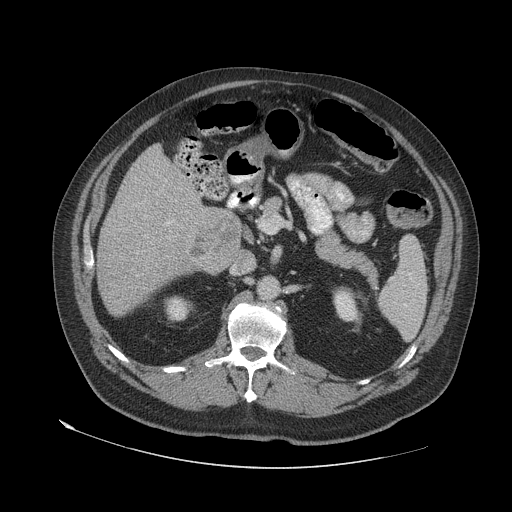
Contrast-enhanced abdominal CT (liver protocol), one axial slice. Reconstruction kernel STANDARD. Soft-tissue window (W 400 / L 40 HU). 2.5 mm slice thickness. 512 × 512 image matrix. Case-level facts recorded for this patient, not image findings: diagnosis: hepatocellular carcinoma (patient treated with transarterial chemoembolisation; whether this scan precedes or follows treatment is not stated here); TNM stage (as recorded): Stage-IVA; Child-Pugh class: A; tumour differentiation: well differentiated; tumour nodularity: multinodular.
Structures marked on this image (semi-automatic segmentation, software-assisted and operator-edited):
- liver parenchyma outside the tumour (the mass and vessels are separate outlines, so this box may not span the whole liver): bounding box <98,146,206,314> (left, top, right, bottom; pixels)
- liver vessels: <166,221,173,225>